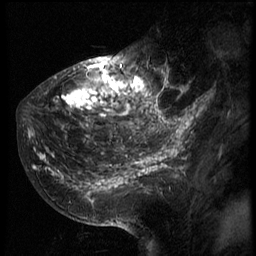
Breast MRI (dynamic contrast-enhanced), one sagittal slice; slice 26 of 66 in the series (ordered by position); 3 images stored at this slice position (order not interpretable as contrast timing); 1.5 T; TE 4.2 ms, TR 8.9 ms; 2.5 mm slice thickness; 256 × 256 image matrix, field of view 200 × 200 mm. Patient: female, 39 years. Case-level facts recorded for this patient, not image findings: setting: breast cancer imaged before/during neoadjuvant chemotherapy; receptor status: HER2-positive.
Structures marked on this image (semi-automatic segmentation, software-assisted and operator-edited):
- analysis volume of interest (the breast-tissue region the enhancement analysis was run in; not a lesion): bounding box (x1, y1, x2, y2) in pixels: (29, 44, 166, 196)
- tumour enhancement mask (voxels above the 140 % enhancement threshold inside the analysis volume of interest): (29, 63, 166, 190)